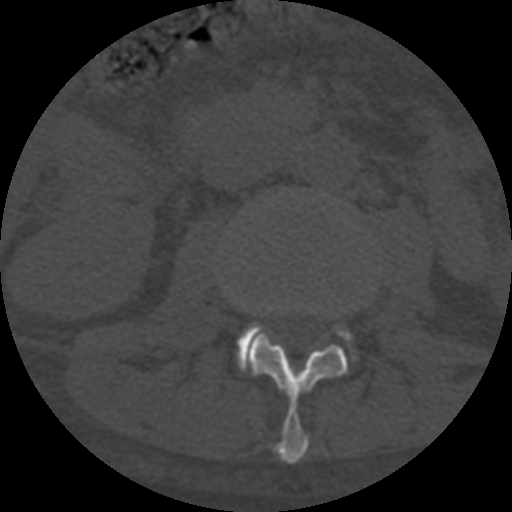
CT including the spine, one axial slice; position 249 of 708 along the scan axis; 120 kVp; one of 3 acquisitions stored at this slice position; bone window (W 1800 / L 400 HU); 512 × 512 image matrix, field of view 160 × 160 mm. Patient age 55 years. Case-level facts recorded for this patient, not image findings: primary cancer: colon.
Structures marked on this image (semi-automatically segmented with operator editing):
- L2 vertebra: box from (x=247, y=304) to (x=348, y=464) px
- L3 vertebra: (x=237, y=325)–(x=263, y=370)